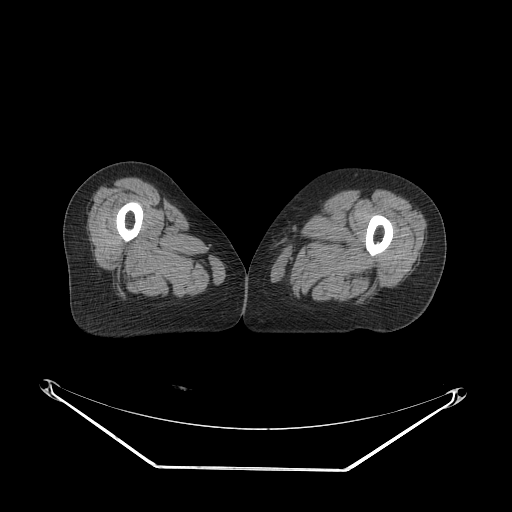
CT of an extremity soft-tissue mass (from a PET/CT study), one axial slice. Position 55 of 91 along the scan axis. Soft-tissue window (W 400 / L 40 HU). 3.75 mm slice thickness. 512 × 512 image matrix, field of view 500 × 500 mm. Female patient. From the clinical record (not read from this slice): histological type: pleomorphic leiomyosarcoma; grade: high; site of the primary tumour: left thigh.
Outlined on this slice (expert contour drawn on MRI and transferred to this co-registered scan by the dataset authors):
- gross tumour volume including surrounding oedema: box from (x=278, y=203) to (x=303, y=229) px